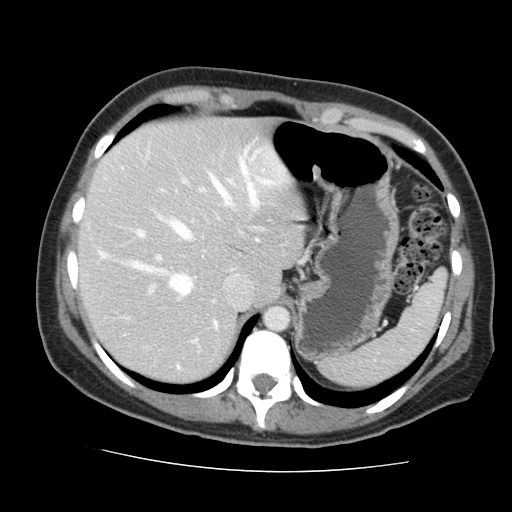
Contrast-enhanced abdominal CT, one axial slice. Position 113 of 144 along the scan axis. 120 kVp. Soft-tissue window (W 400 / L 40 HU). 2.5 mm slice thickness. 512 × 512 image matrix. Female patient, age 46 years. Case-level facts recorded for this patient, not image findings: diagnosis: colorectal cancer liver metastases, imaged before liver resection.
Structures marked on this image (outlined manually by an expert reader):
- hepatic veins: bounding box [x1, y1, x2, y2] px = [101, 159, 258, 296]
- liver: [80, 119, 300, 381]
- planned liver remnant (the part of the liver to remain after resection): [80, 119, 300, 381]
- portal vein (with intrahepatic branches): [98, 178, 236, 369]